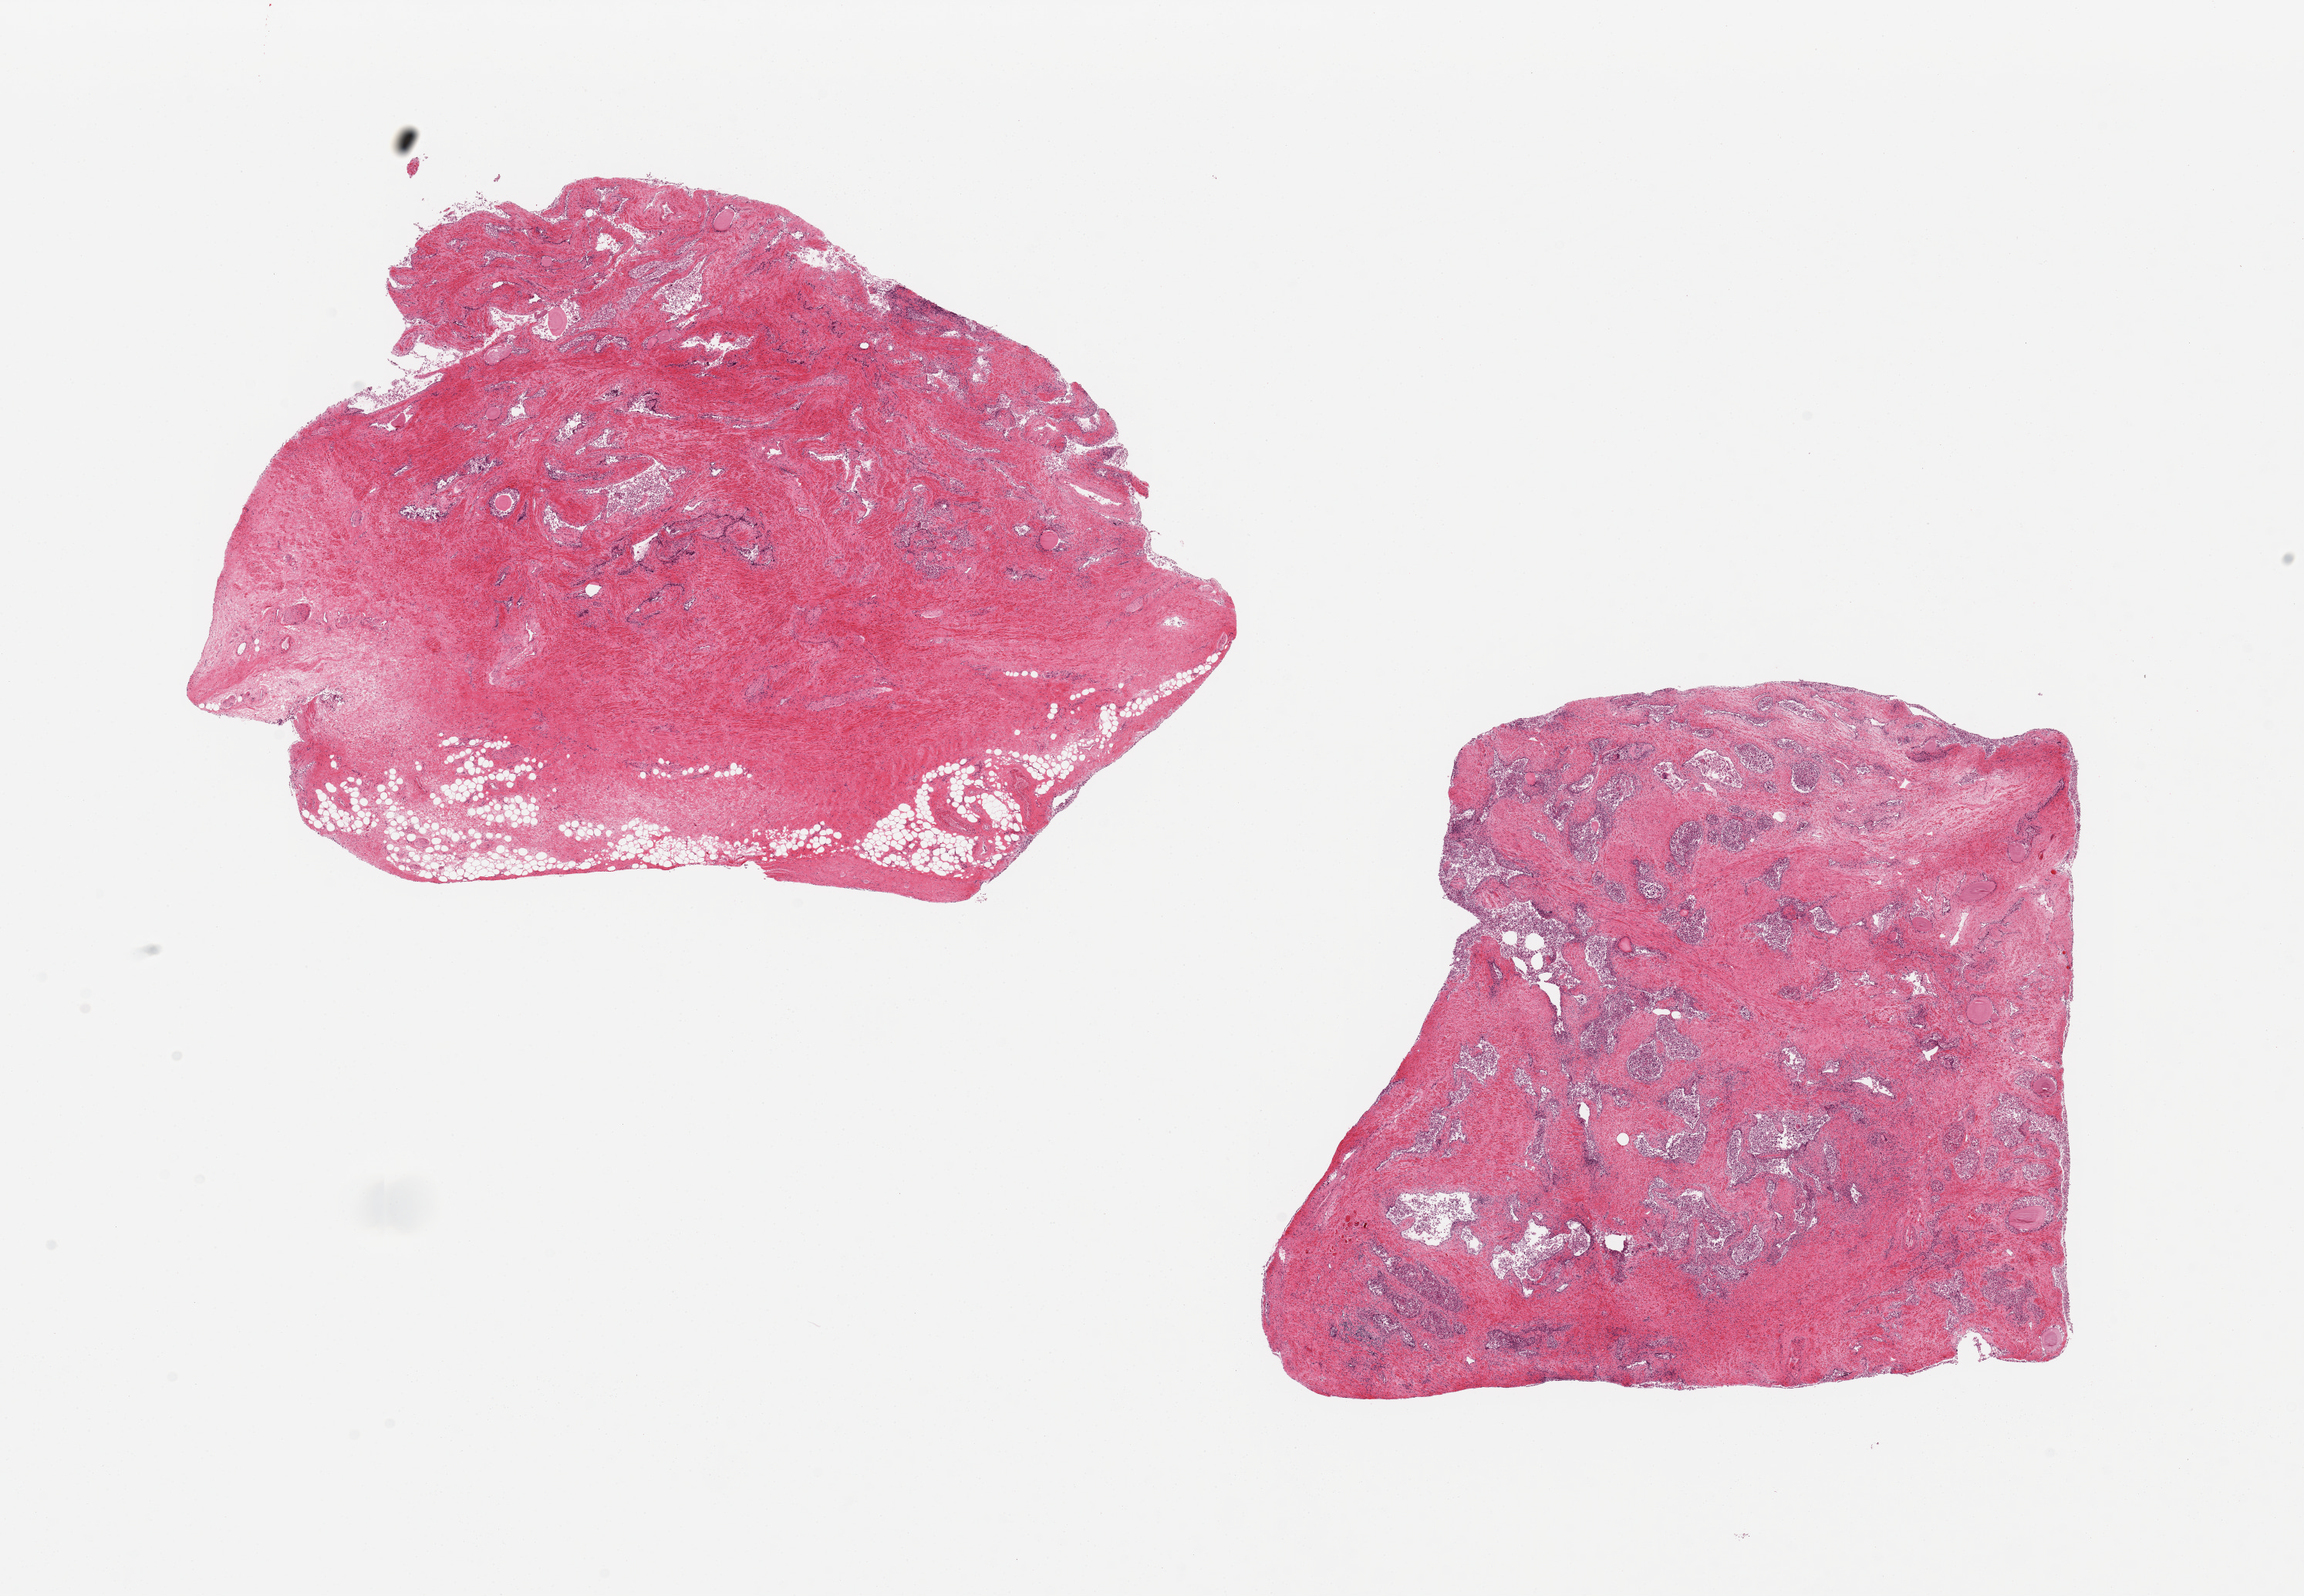
Digitized hematoxylin and eosin (H&E)-stained section, a low-resolution overview of the entire scanned area, about 23.6 x 16.4 mm (acquisition: 20x scan), PAXgene-fixed, paraffin-embedded tissue, target tissue: prostate, tissue donor sample. Donor: male.
Review note (as recorded): 2 pieces, markedly autolyzed glandular component.